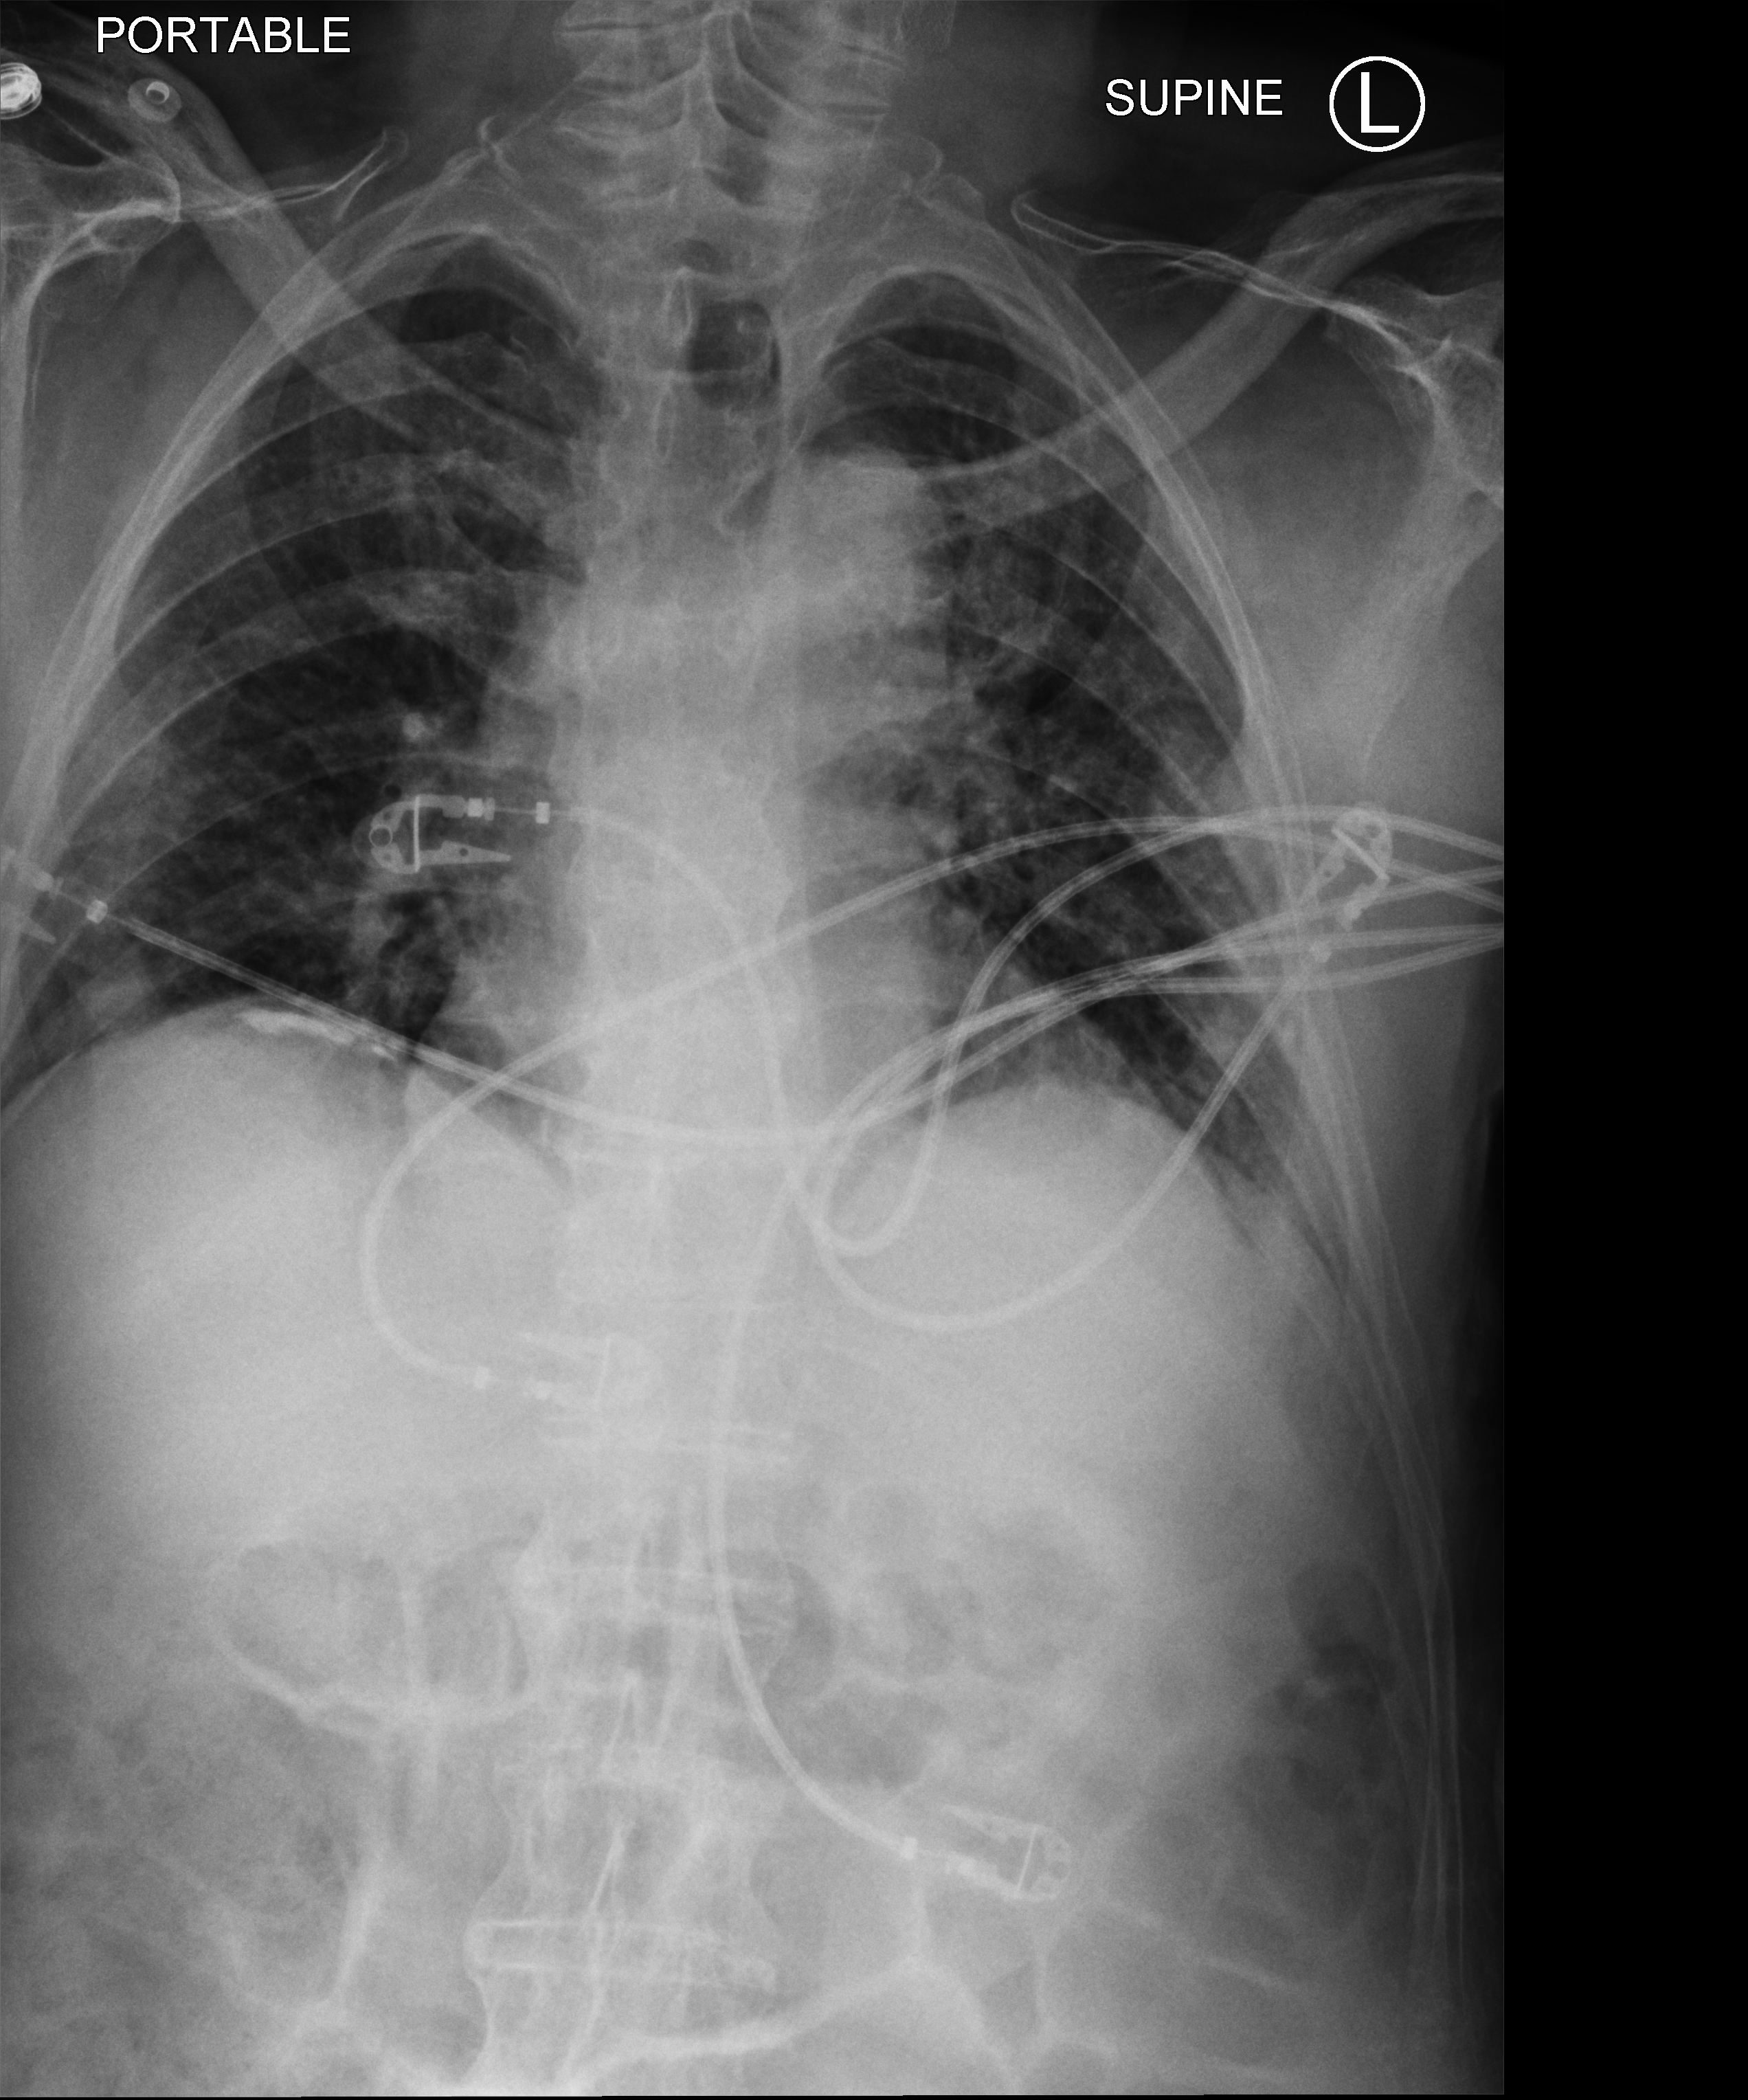
Bedside chest radiograph (computed radiography); anteroposterior (AP) projection. Male patient hospitalised with COVID-19, age 75–90 years.
From the hospital-stay record, not from the radiograph (when in the stay this image was taken is not recorded): admitted to intensive care during this hospital stay: no; length of hospital stay: 1 day.